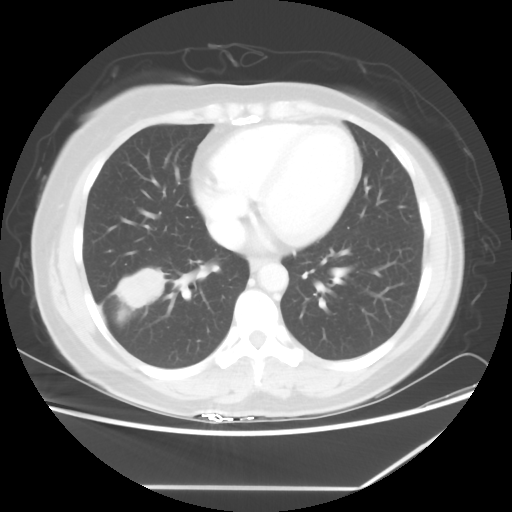
Chest CT, one axial slice. Slice 24 of 60 in the series (ordered by position). 100 kVp. Lung window (W 1500 / L -600 HU). 512 × 512 image matrix. Female patient, age 42 years. From the clinical record (not read from this slice): clinical TNM (as recorded): T2 N1 M0.
Outlined on this slice (bounding box drawn by a radiologist):
- lung tumour (recorded histology: adenocarcinoma): bounding box <108,263,168,313> (left, top, right, bottom; pixels)